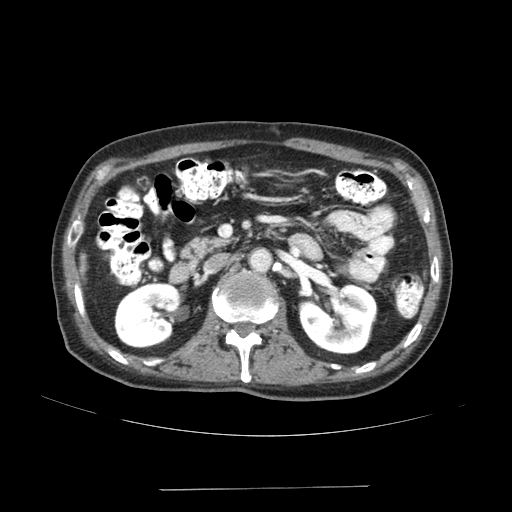
Contrast-enhanced abdominal CT (liver protocol), one axial slice; position 52 of 192 along the scan axis; reconstruction kernel SOFT; soft-tissue window (W 400 / L 40 HU); 2.5 mm slice thickness; 512 × 512 image matrix. Case-level facts recorded for this patient, not image findings: diagnosis: hepatocellular carcinoma (patient treated with transarterial chemoembolisation; whether this scan precedes or follows treatment is not stated here); TNM stage (as recorded): Stage-IVA; Child-Pugh class: A; tumour differentiation: poorly differentiated.
Annotated regions visible in this slice (semi-automatically segmented with operator editing):
- liver parenchyma outside the tumour (the mass and vessels are separate outlines, so this box may not span the whole liver): bounding box [x1, y1, x2, y2] px = [80, 253, 86, 272]